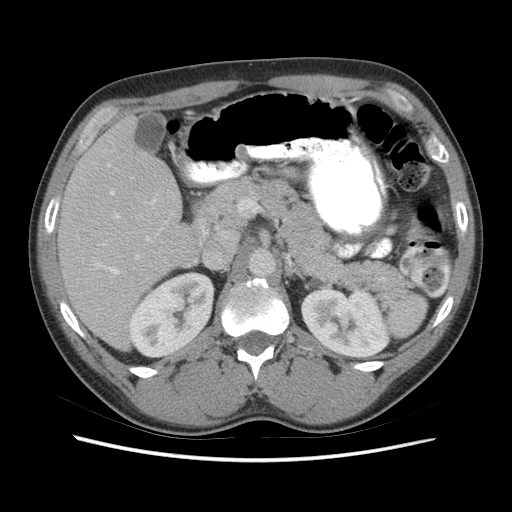
Contrast-enhanced abdominal CT (liver protocol), one axial slice; slice 31 of 73 in the series (ordered by position); 140 kVp; soft-tissue window (W 400 / L 40 HU); 2.5 mm slice thickness; 512 × 512 image matrix, field of view 360 × 360 mm. From the clinical record (not read from this slice): diagnosis: hepatocellular carcinoma (patient treated with transarterial chemoembolisation; whether this scan precedes or follows treatment is not stated here); TNM stage (as recorded): Stage-IIIA; Child-Pugh class: A; tumour nodularity: multinodular; tumour size: 6.6 cm.
Structures marked on this image (semi-automatic segmentation, software-assisted and operator-edited):
- liver parenchyma outside the tumour (the mass and vessels are separate outlines, so this box may not span the whole liver): bounding box (x1, y1, x2, y2) in pixels: (58, 114, 211, 348)
- liver vessels: (95, 165, 206, 275)